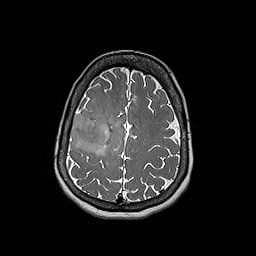
Brain MRI from a brain-tumour surgery series, one axial slice. Position 61 of 192 along the scan axis. 1 mm slice thickness. 256 × 256 image matrix. Case-level facts recorded for this patient, not image findings: histopathology: Oligodendroglioma; WHO grade: 3; IDH mutation: yes; tumour location: Right Frontal.
Outlined on this slice (manually delineated by an expert):
- tumour: bounding box <69,115,108,153> (left, top, right, bottom; pixels)